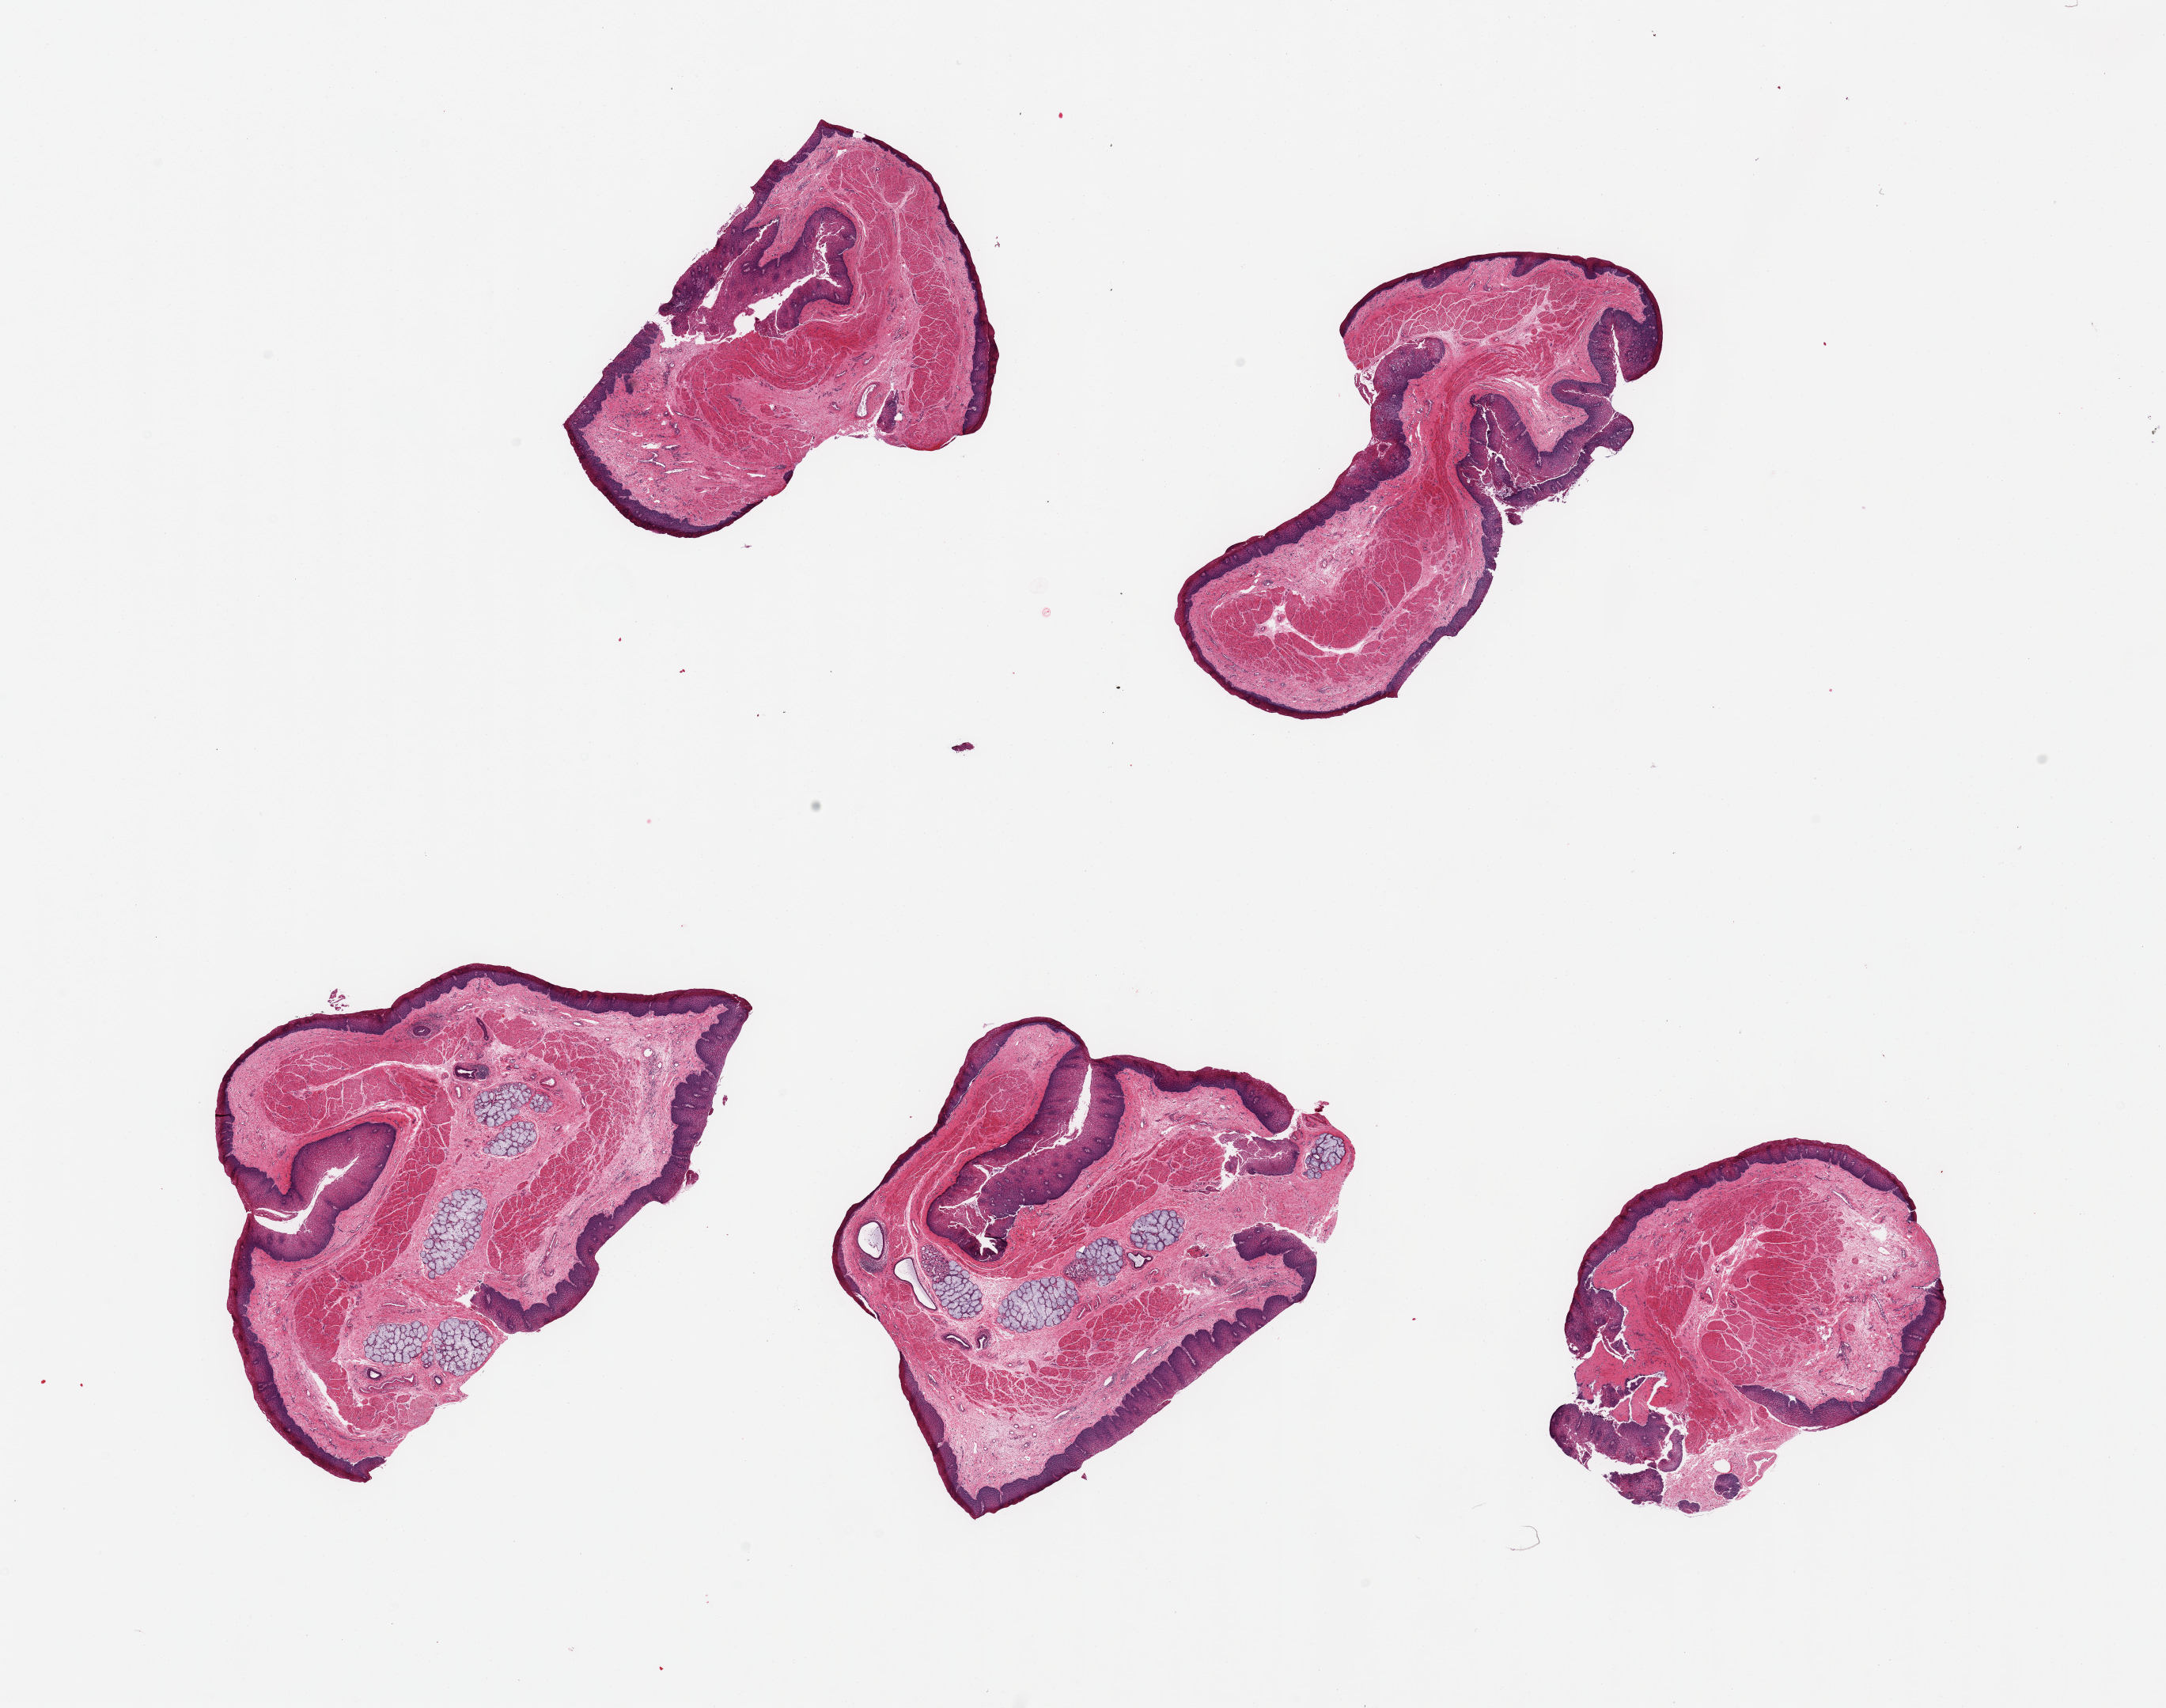
Whole-slide image, haematoxylin and eosin stain — shown as a low-resolution overview of the whole scanned area (about 21.7 x 17.1 mm, acquisition: 20x scan); PAXgene-fixed, paraffin-embedded tissue; sampled site (target tissue): esophageal mucous membrane; donor tissue sample. Donor sex: female.
Pathologist's review note for this sample: 5 pieces; 2 with prominent submucosal glands [10%].